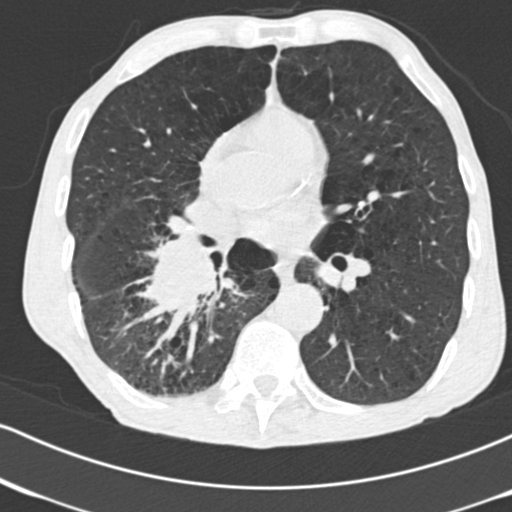
Chest CT (low-dose screening protocol), one axial image, second screening round (one year after baseline), lung window (W 1500 / L -600 HU), 2 mm slice thickness, slice 100 of 182 in the series, 512 × 512 image matrix. Male, age 64 years at enrolment. Current smoker at enrolment.
Expert-annotated lung lesion, bounding box <127,227,241,335> (left, top, right, bottom; pixels). Screening reader's record for this exam (one nodule recorded; not confirmed to be the boxed lesion): non-calcified nodule or mass ≥4 mm, 52 × 37 mm, spiculated (stellate) margins, soft tissue attenuation, pre-existing on the prior screen: no. Official screen result: positive, other. Later outcome: lung cancer diagnosed 28 days after this screen — adenocarcinoma, NOS, right lower lobe, stage IV (AJCC 6th edition), 60 mm at pathology.